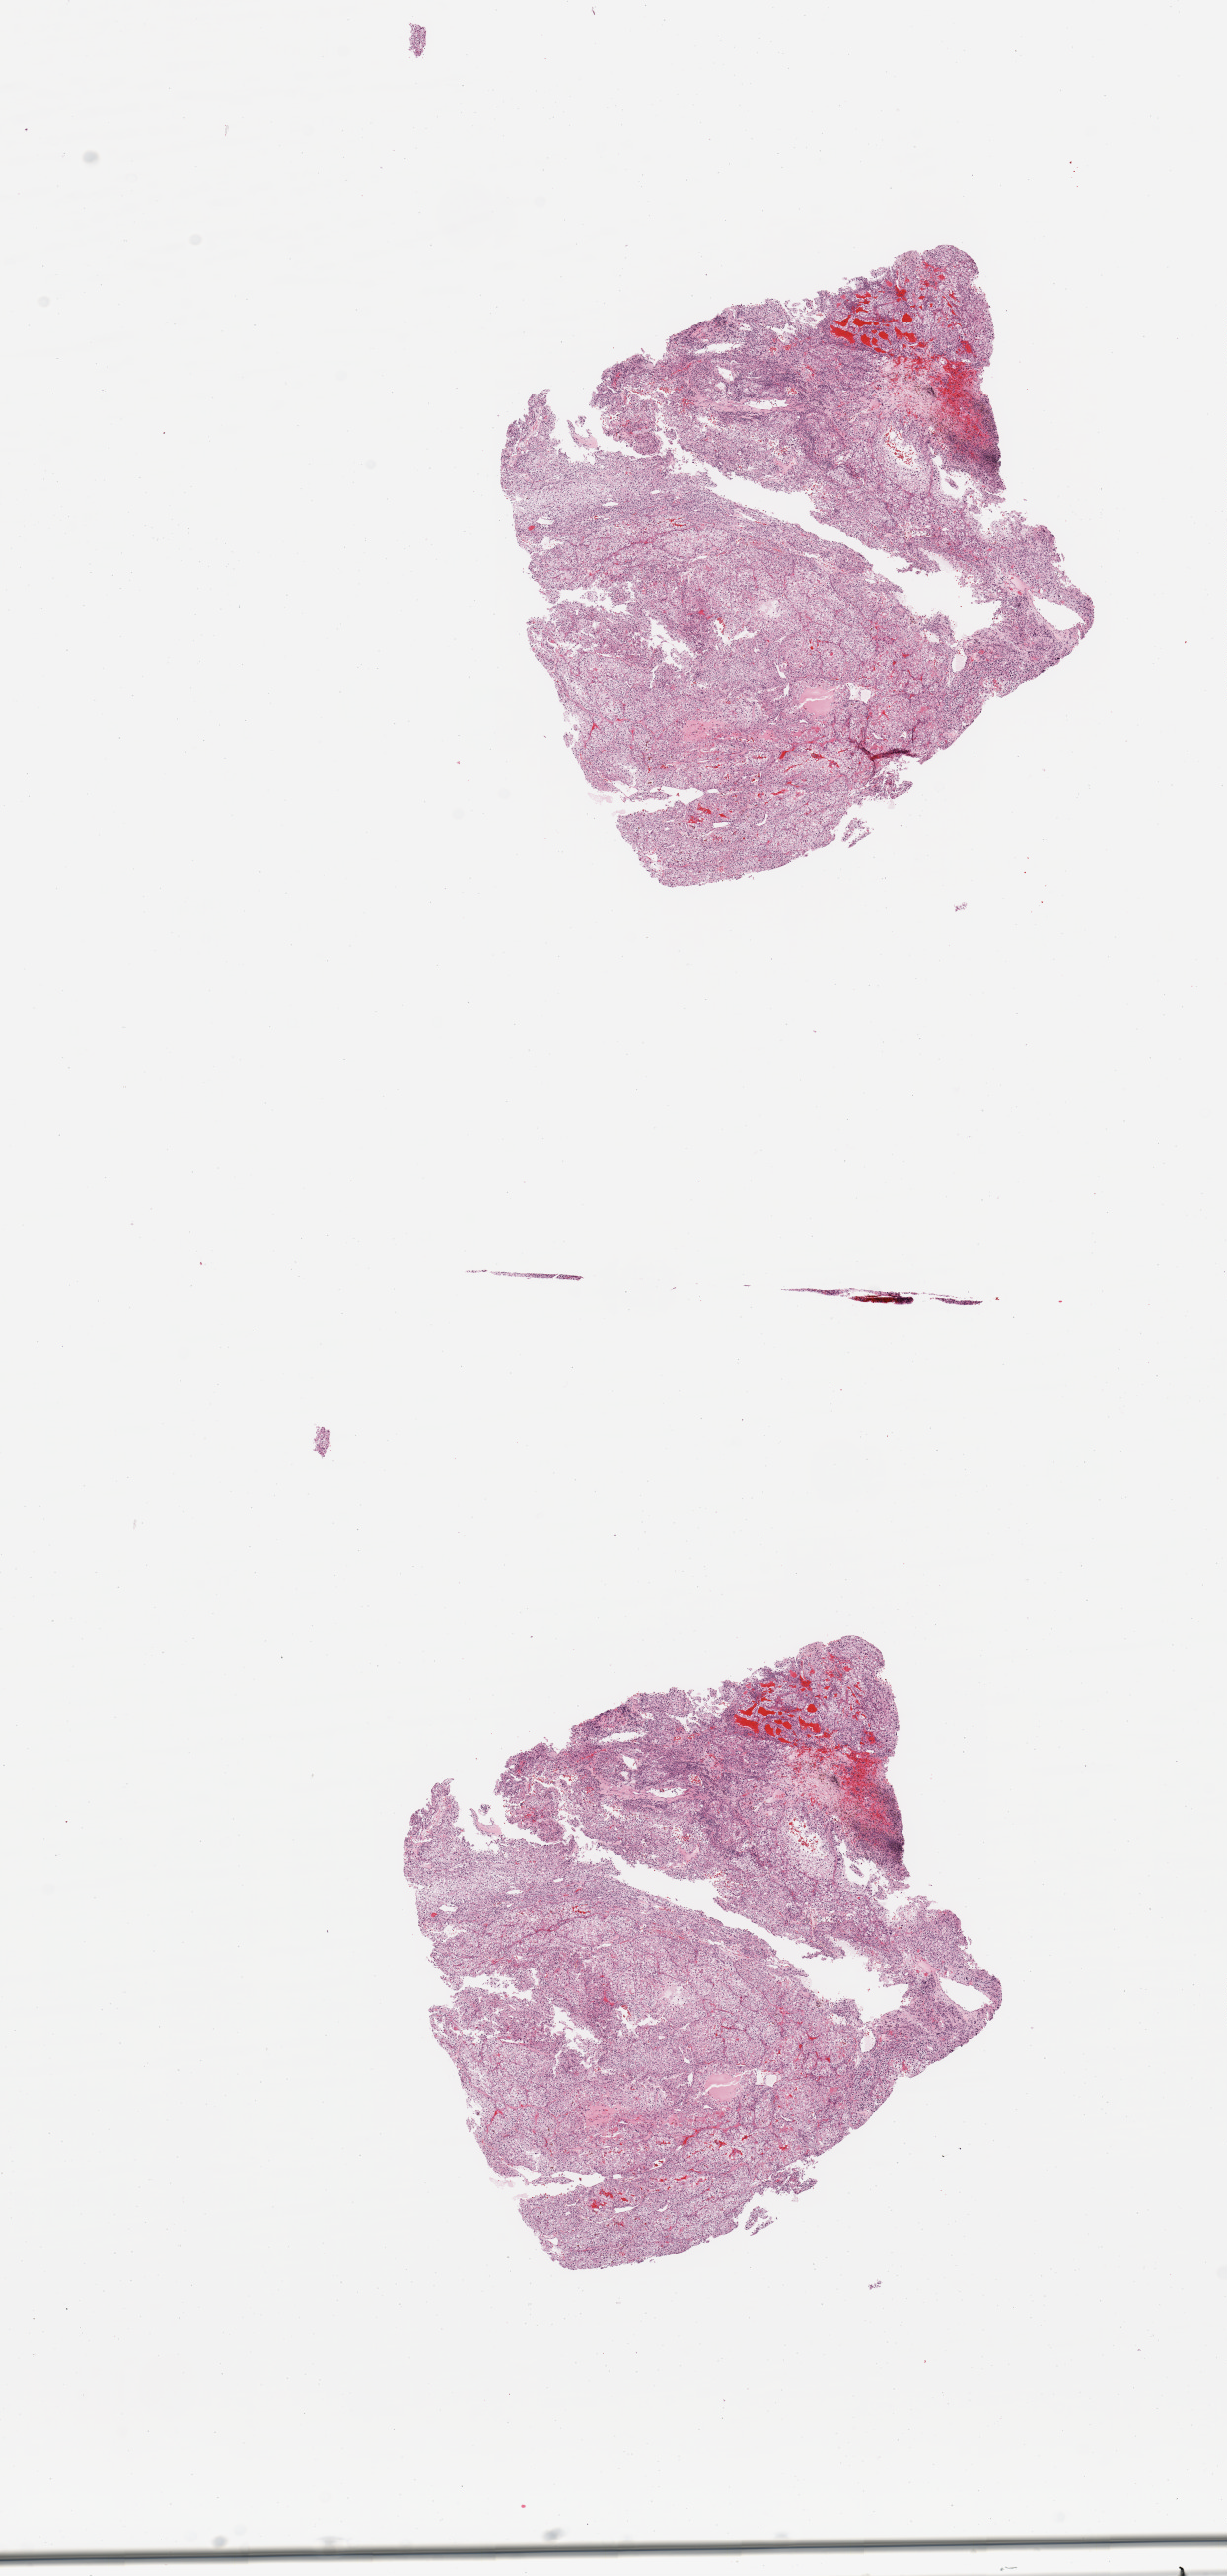
Whole-slide histology image, Hematoxylin and eosin (H&E) stained, shown as a low-resolution overview of the whole scanned area (about 9.8 x 20.7 mm); tumour tissue sample, sampled site: kidney. Patient: male, age 83 years. Histologic grade: G3 (poorly differentiated). Composition of this section per pathologist review: tumour nuclei 90%, necrosis 5%.
• AJCC pathologic stage: III
• histologic diagnosis: Renal cell carcinoma, NOS
• primary tumour site (as recorded): lower pole